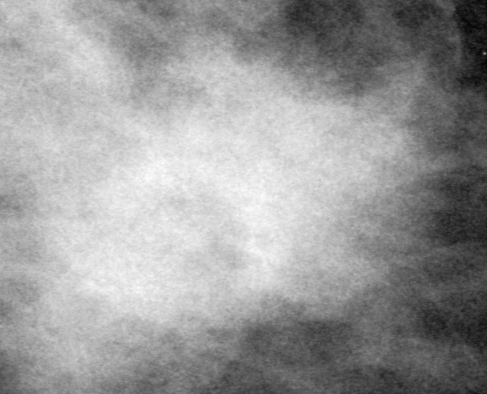
Cropped region of a digitized screen-film mammogram centred on a radiologist-marked abnormality; right breast; CC view; BI-RADS breast density category 2 (scale 1–4).
- Mass, shape irregular, margins ill defined; BI-RADS assessment category 3; subtlety rating 4 on a 1 (subtle) to 5 (obvious) scale; pathology (as recorded): malignant.